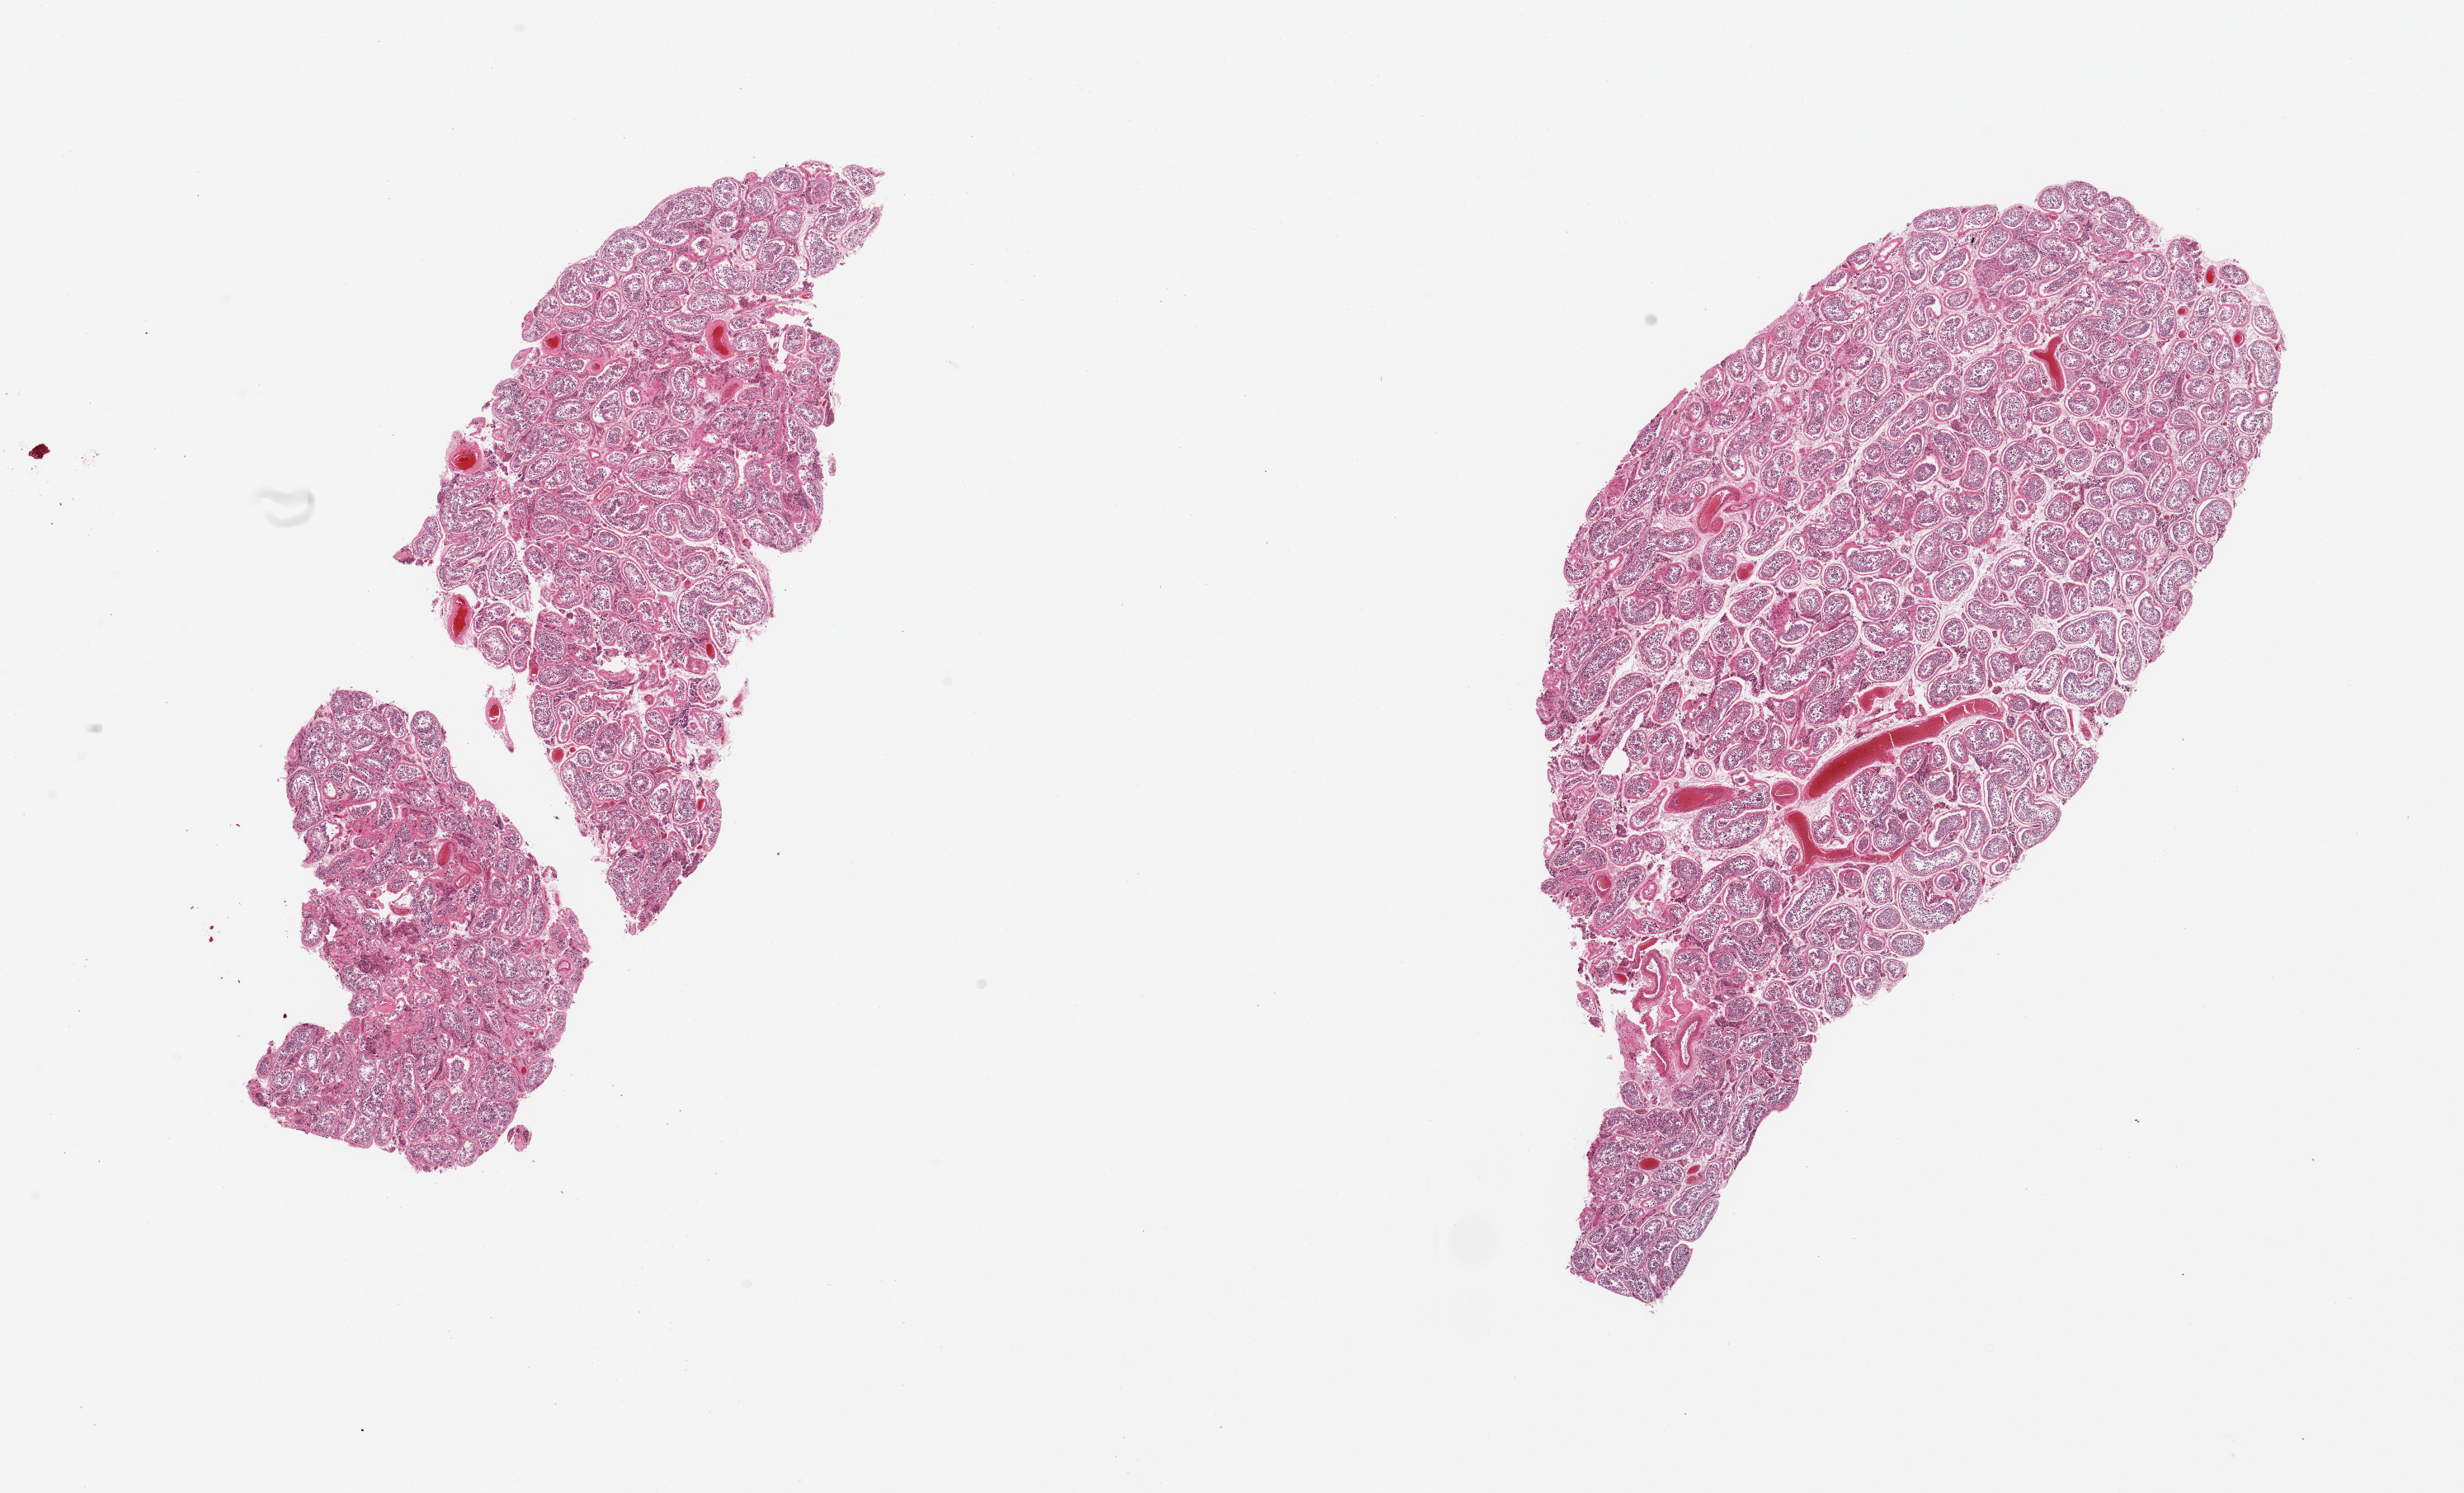
Hematoxylin and eosin (H&E) whole-slide image — whole scanned area (about 23.6 x 14.3 mm, acquisition: 20x scan) shown as a low-resolution overview, PAXgene-fixed paraffin-embedded (PFPE) section, section of testis (target tissue), tissue donor sample. Male donor.
Review note (as recorded): 2 pieces; reduced spermatogenesis.